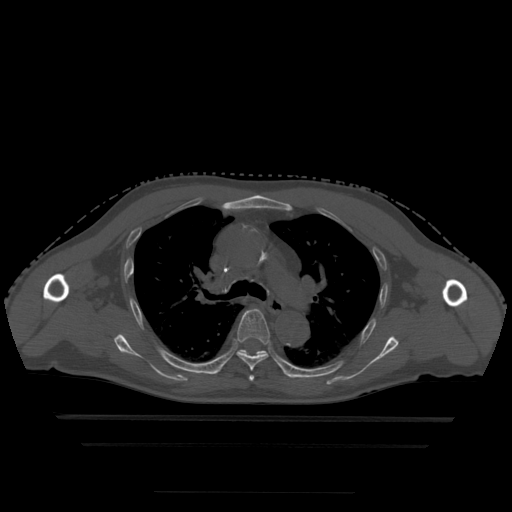
CT including the spine, one axial slice. Position 334 of 522 along the scan axis. Bone window (W 1800 / L 400 HU). 512 × 512 image matrix, field of view 436 × 436 mm. Patient age 68 years. From the clinical record (not read from this slice): primary cancer: urothelial.
Outlined on this slice (semi-automatically segmented with operator editing):
- T4 vertebra: box from (x=249, y=376) to (x=255, y=382) px
- T5 vertebra: (x=237, y=309)–(x=272, y=372)
- T6 vertebra: (x=239, y=350)–(x=267, y=356)